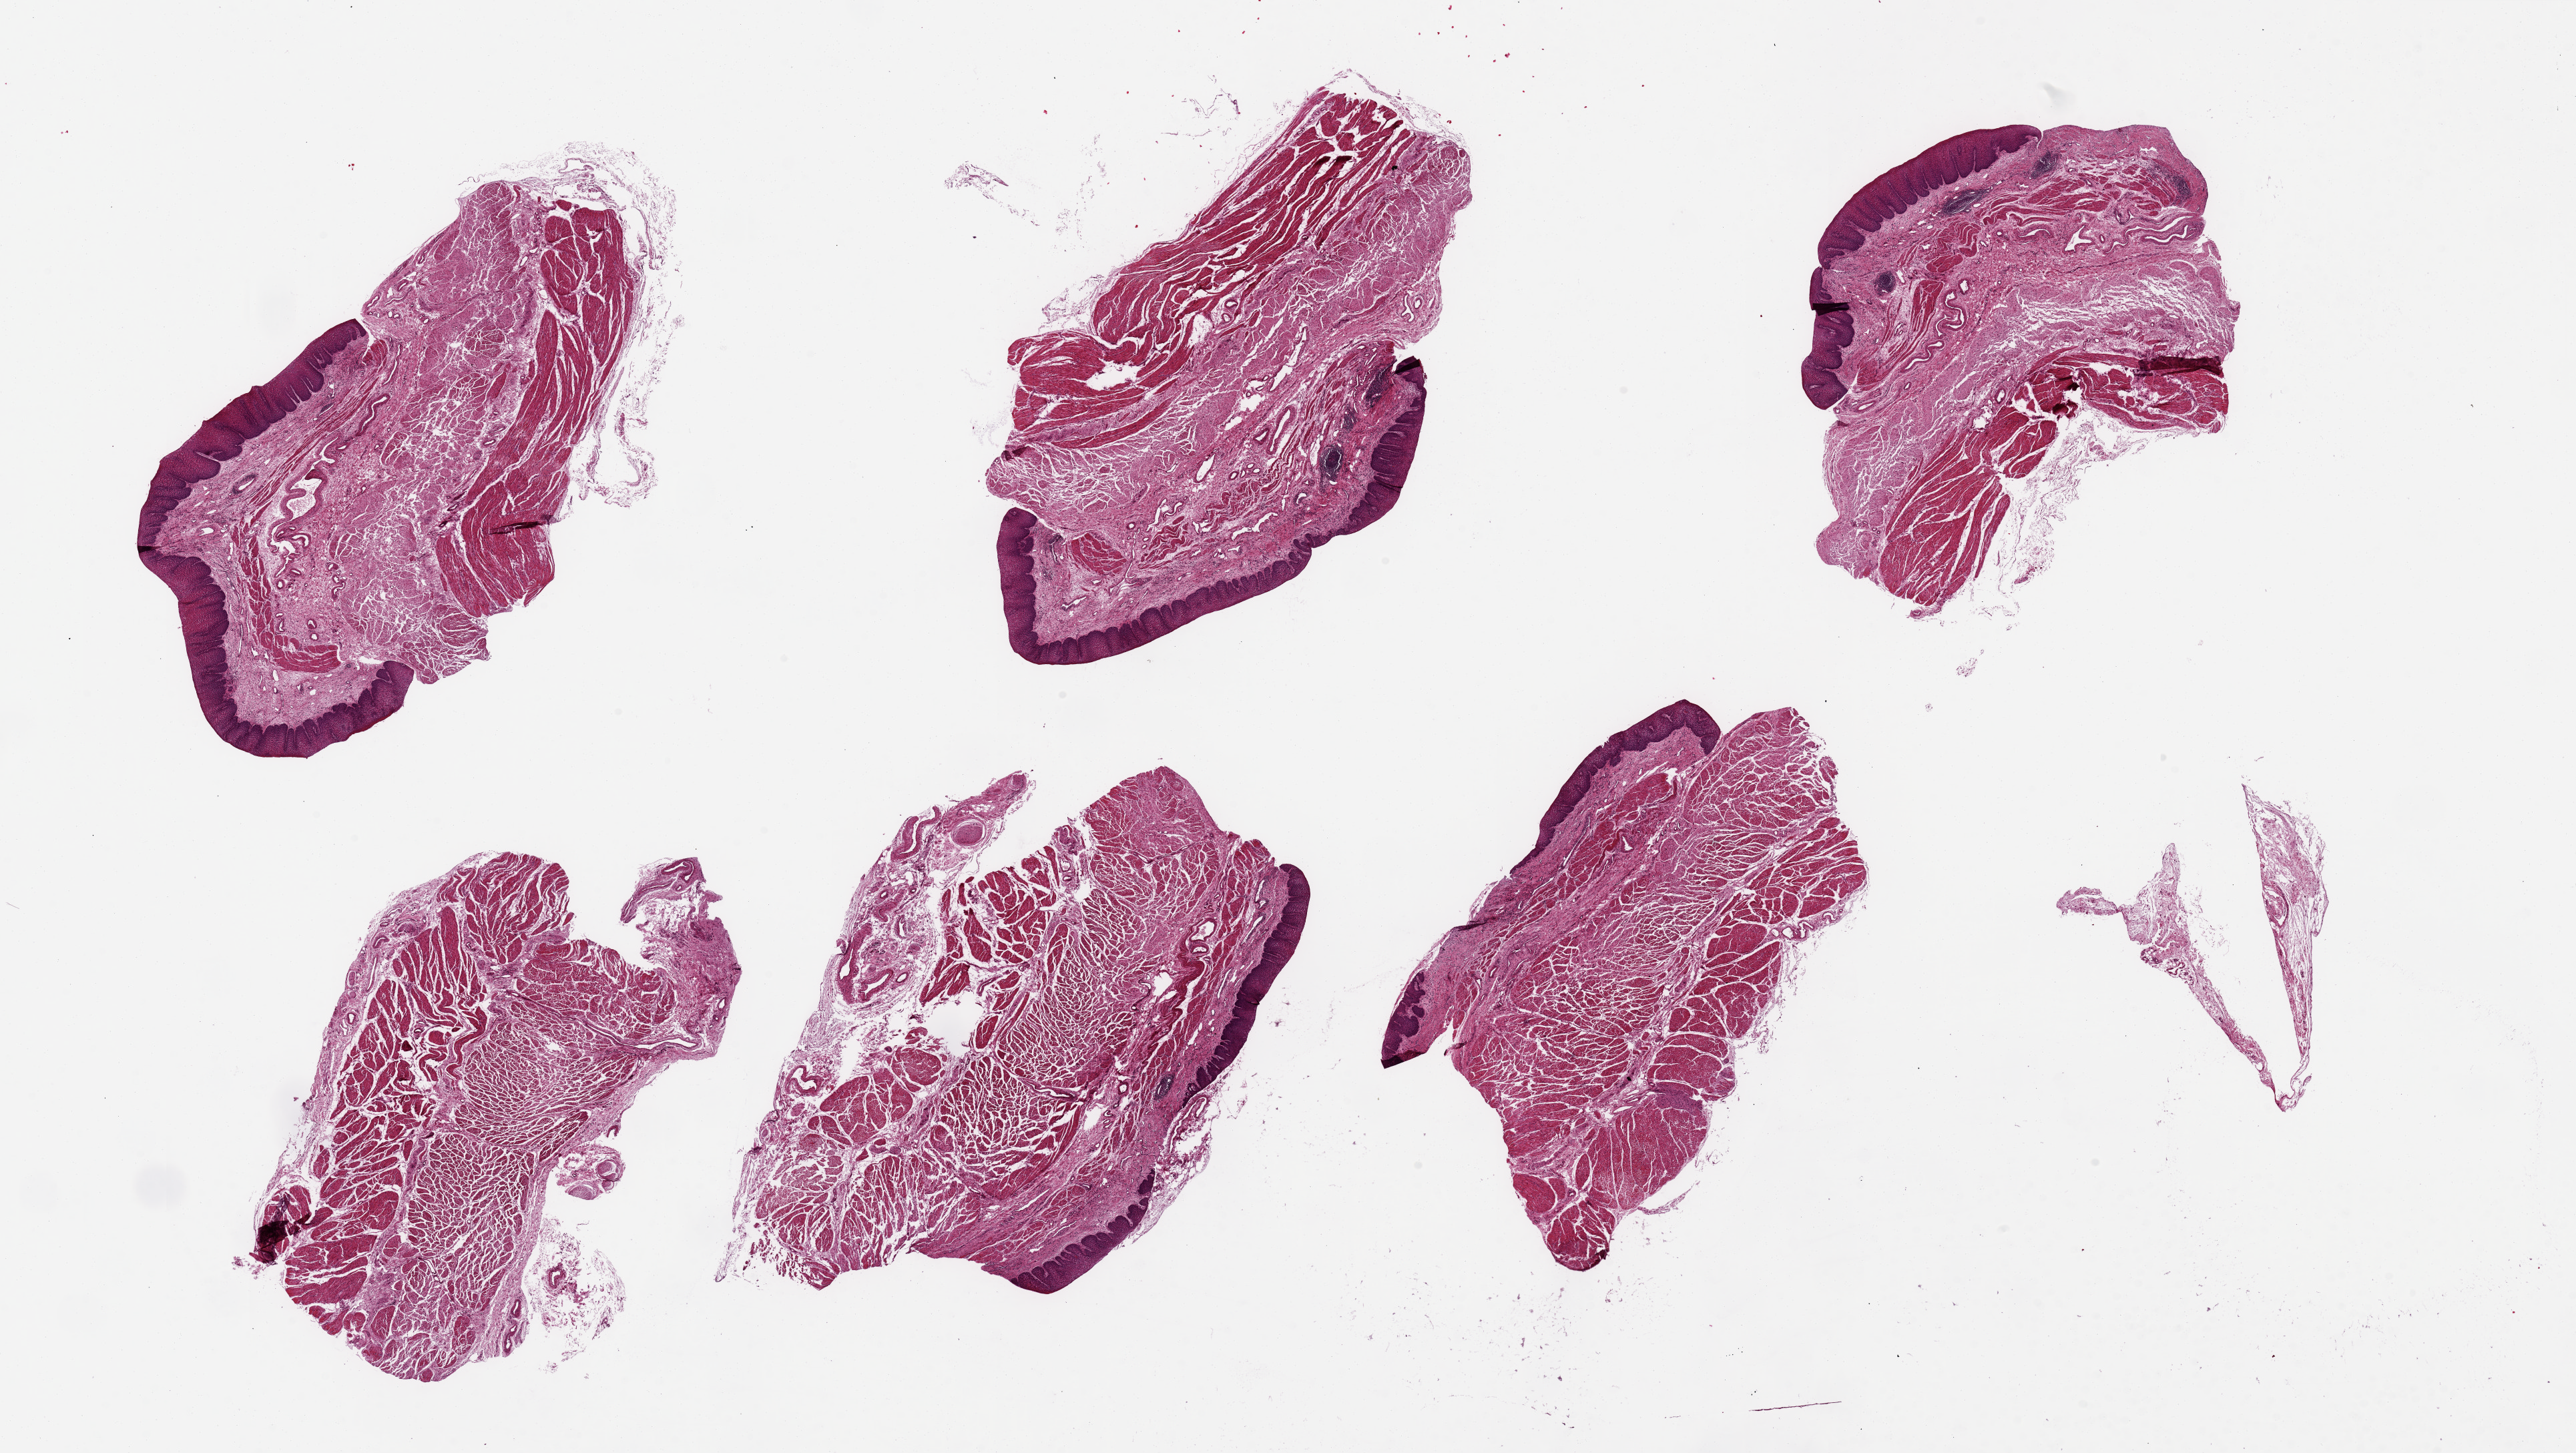
Hematoxylin and eosin (H&E) whole-slide image — low-resolution overview of the scanned area, about 30.5 x 17.2 mm (slide scanned at 20x), PAXgene-fixed, paraffin-embedded tissue, sampled site (target tissue): esophageal muscle, donor tissue sample.
- review note (as recorded): 6 pieces up to 8x4 mm; 5 have mucosa and muscularis propria; 1 has only muscularis